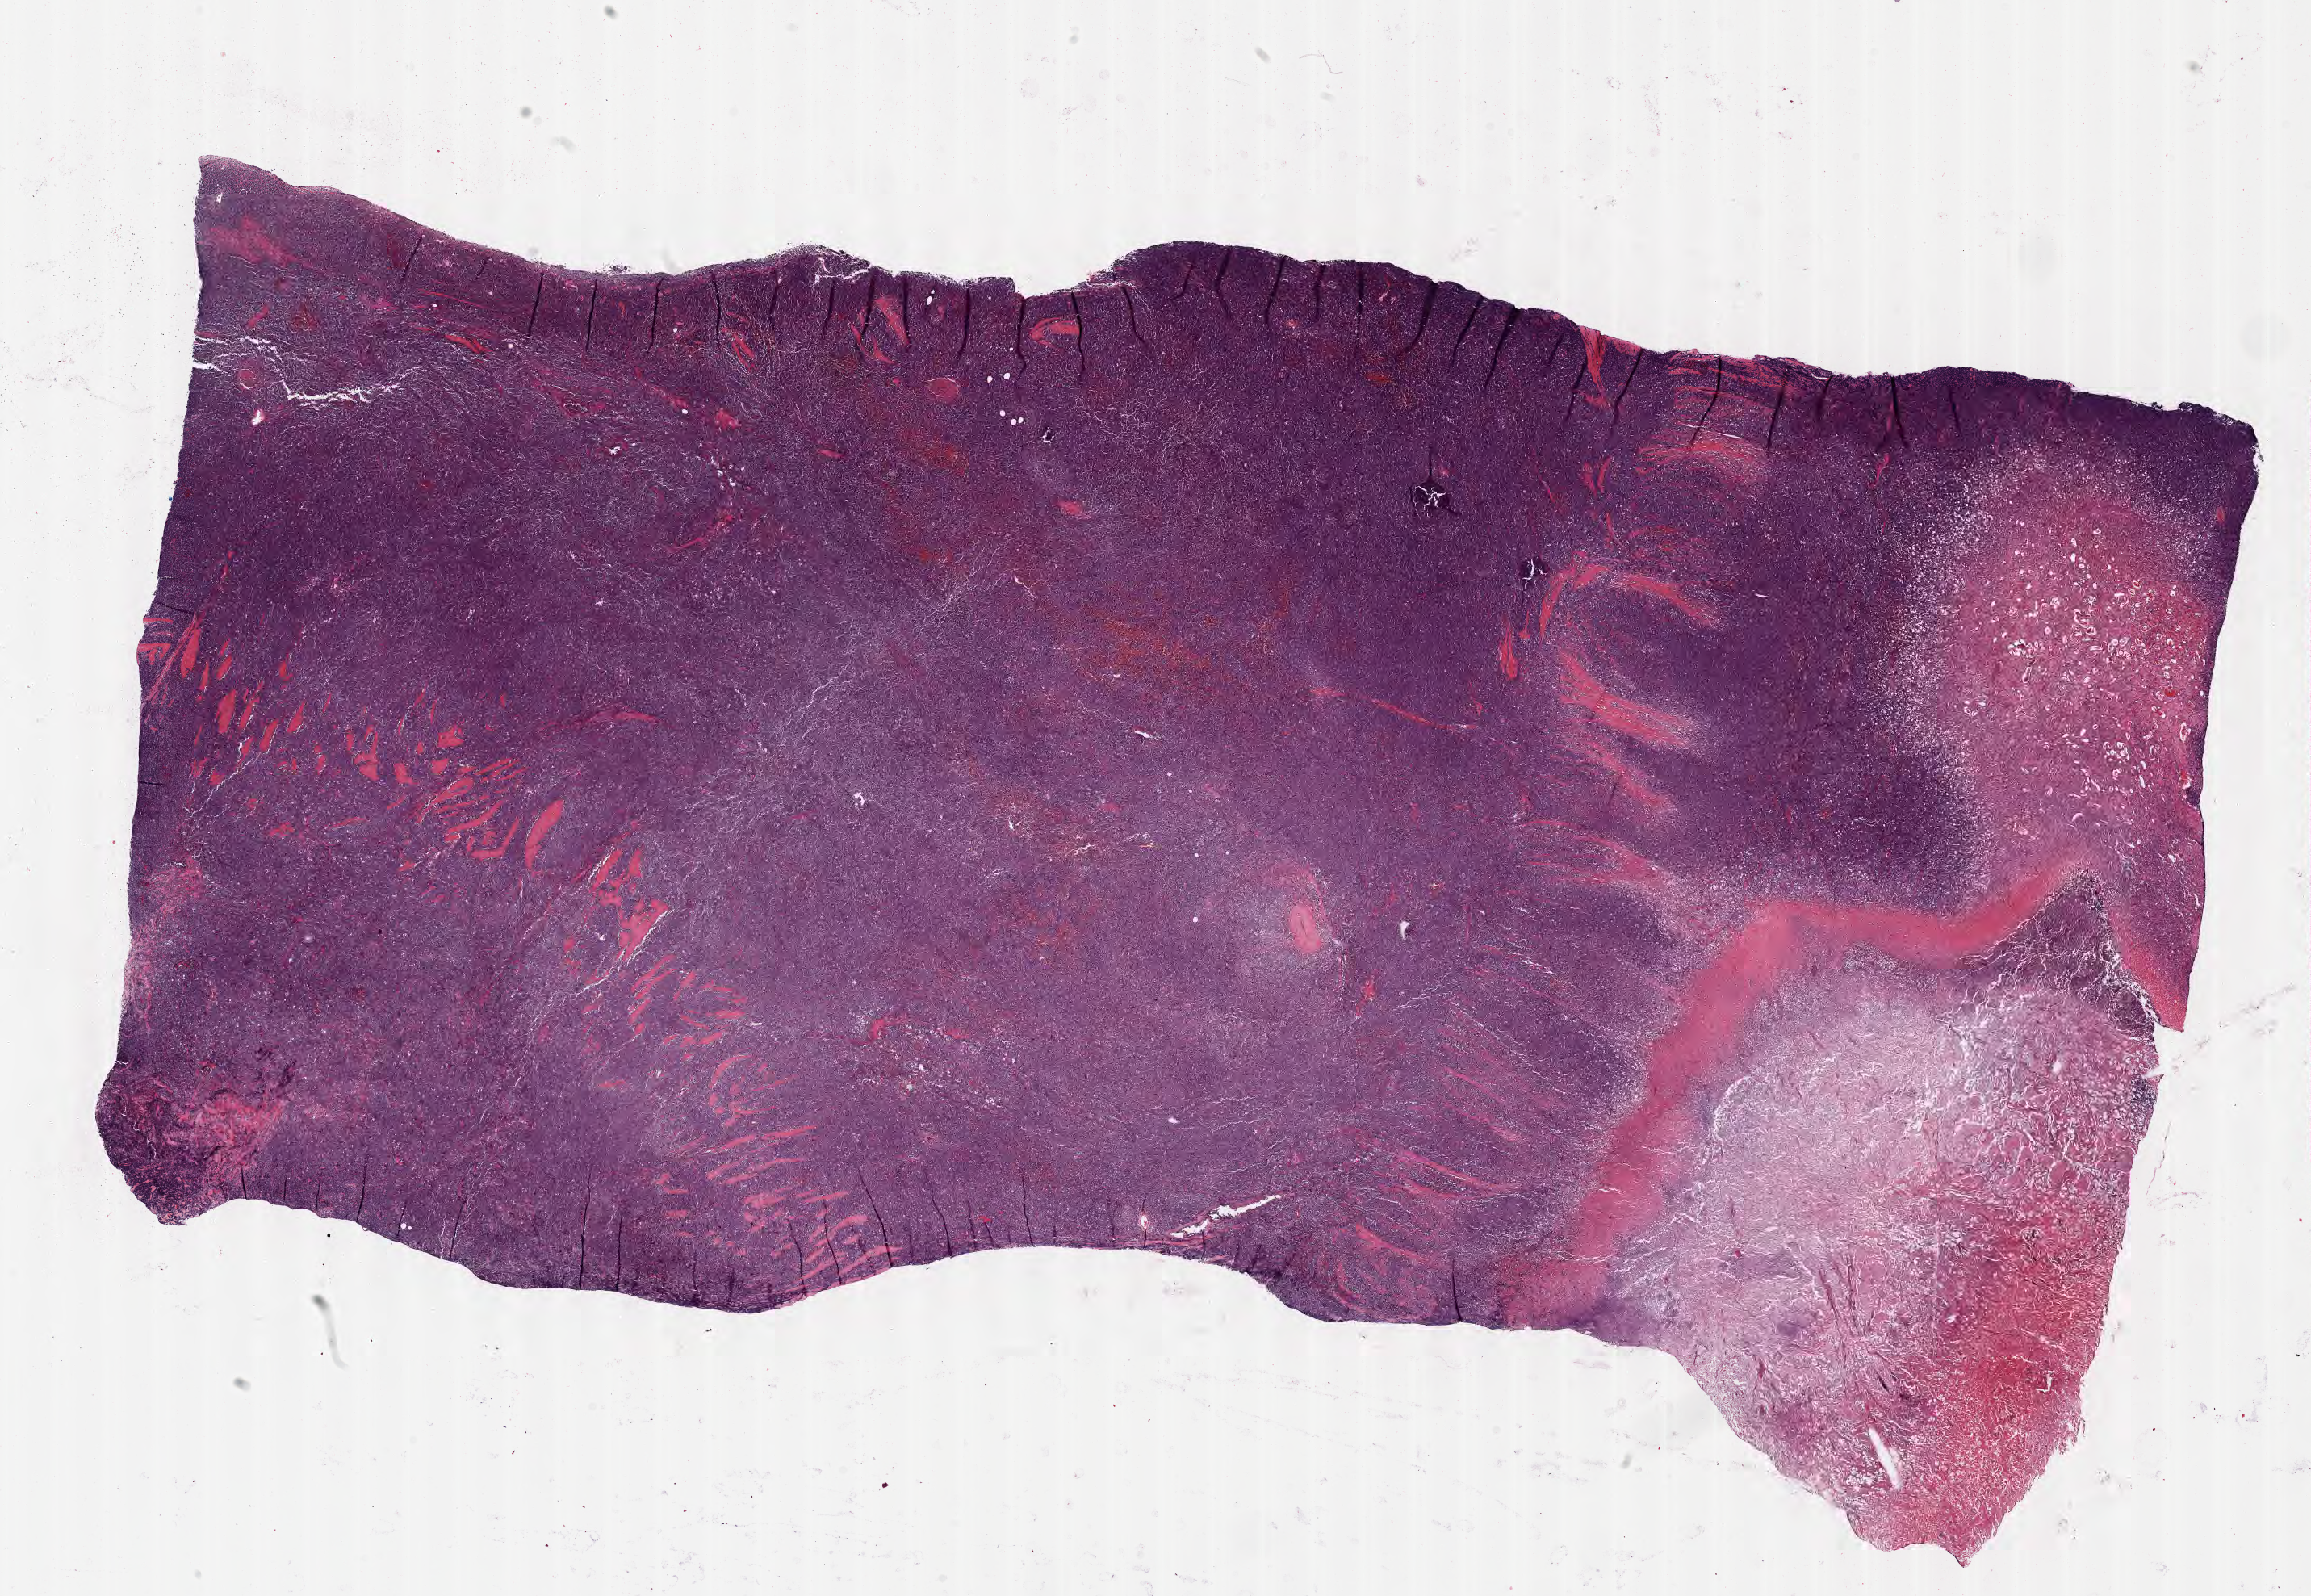
Hematoxylin and eosin (H&E) whole-slide image, low-resolution overview of the scanned area, about 23.1 x 16.0 mm. FFPE section. Specimen: primary tumor. Male patient, 59 years old. Composition of this section per pathologist review: tumor cells 70%, tumor nuclei 90%, stromal cells 10%, necrosis 20%, normal cells 0%. Infiltration values recorded for this section: lymphocyte infiltration 60%, monocyte infiltration 30%, neutrophil infiltration 5%.
Ann Arbor stage (patient): Stage I. Histologic diagnosis: Burkitt lymphoma, NOS.